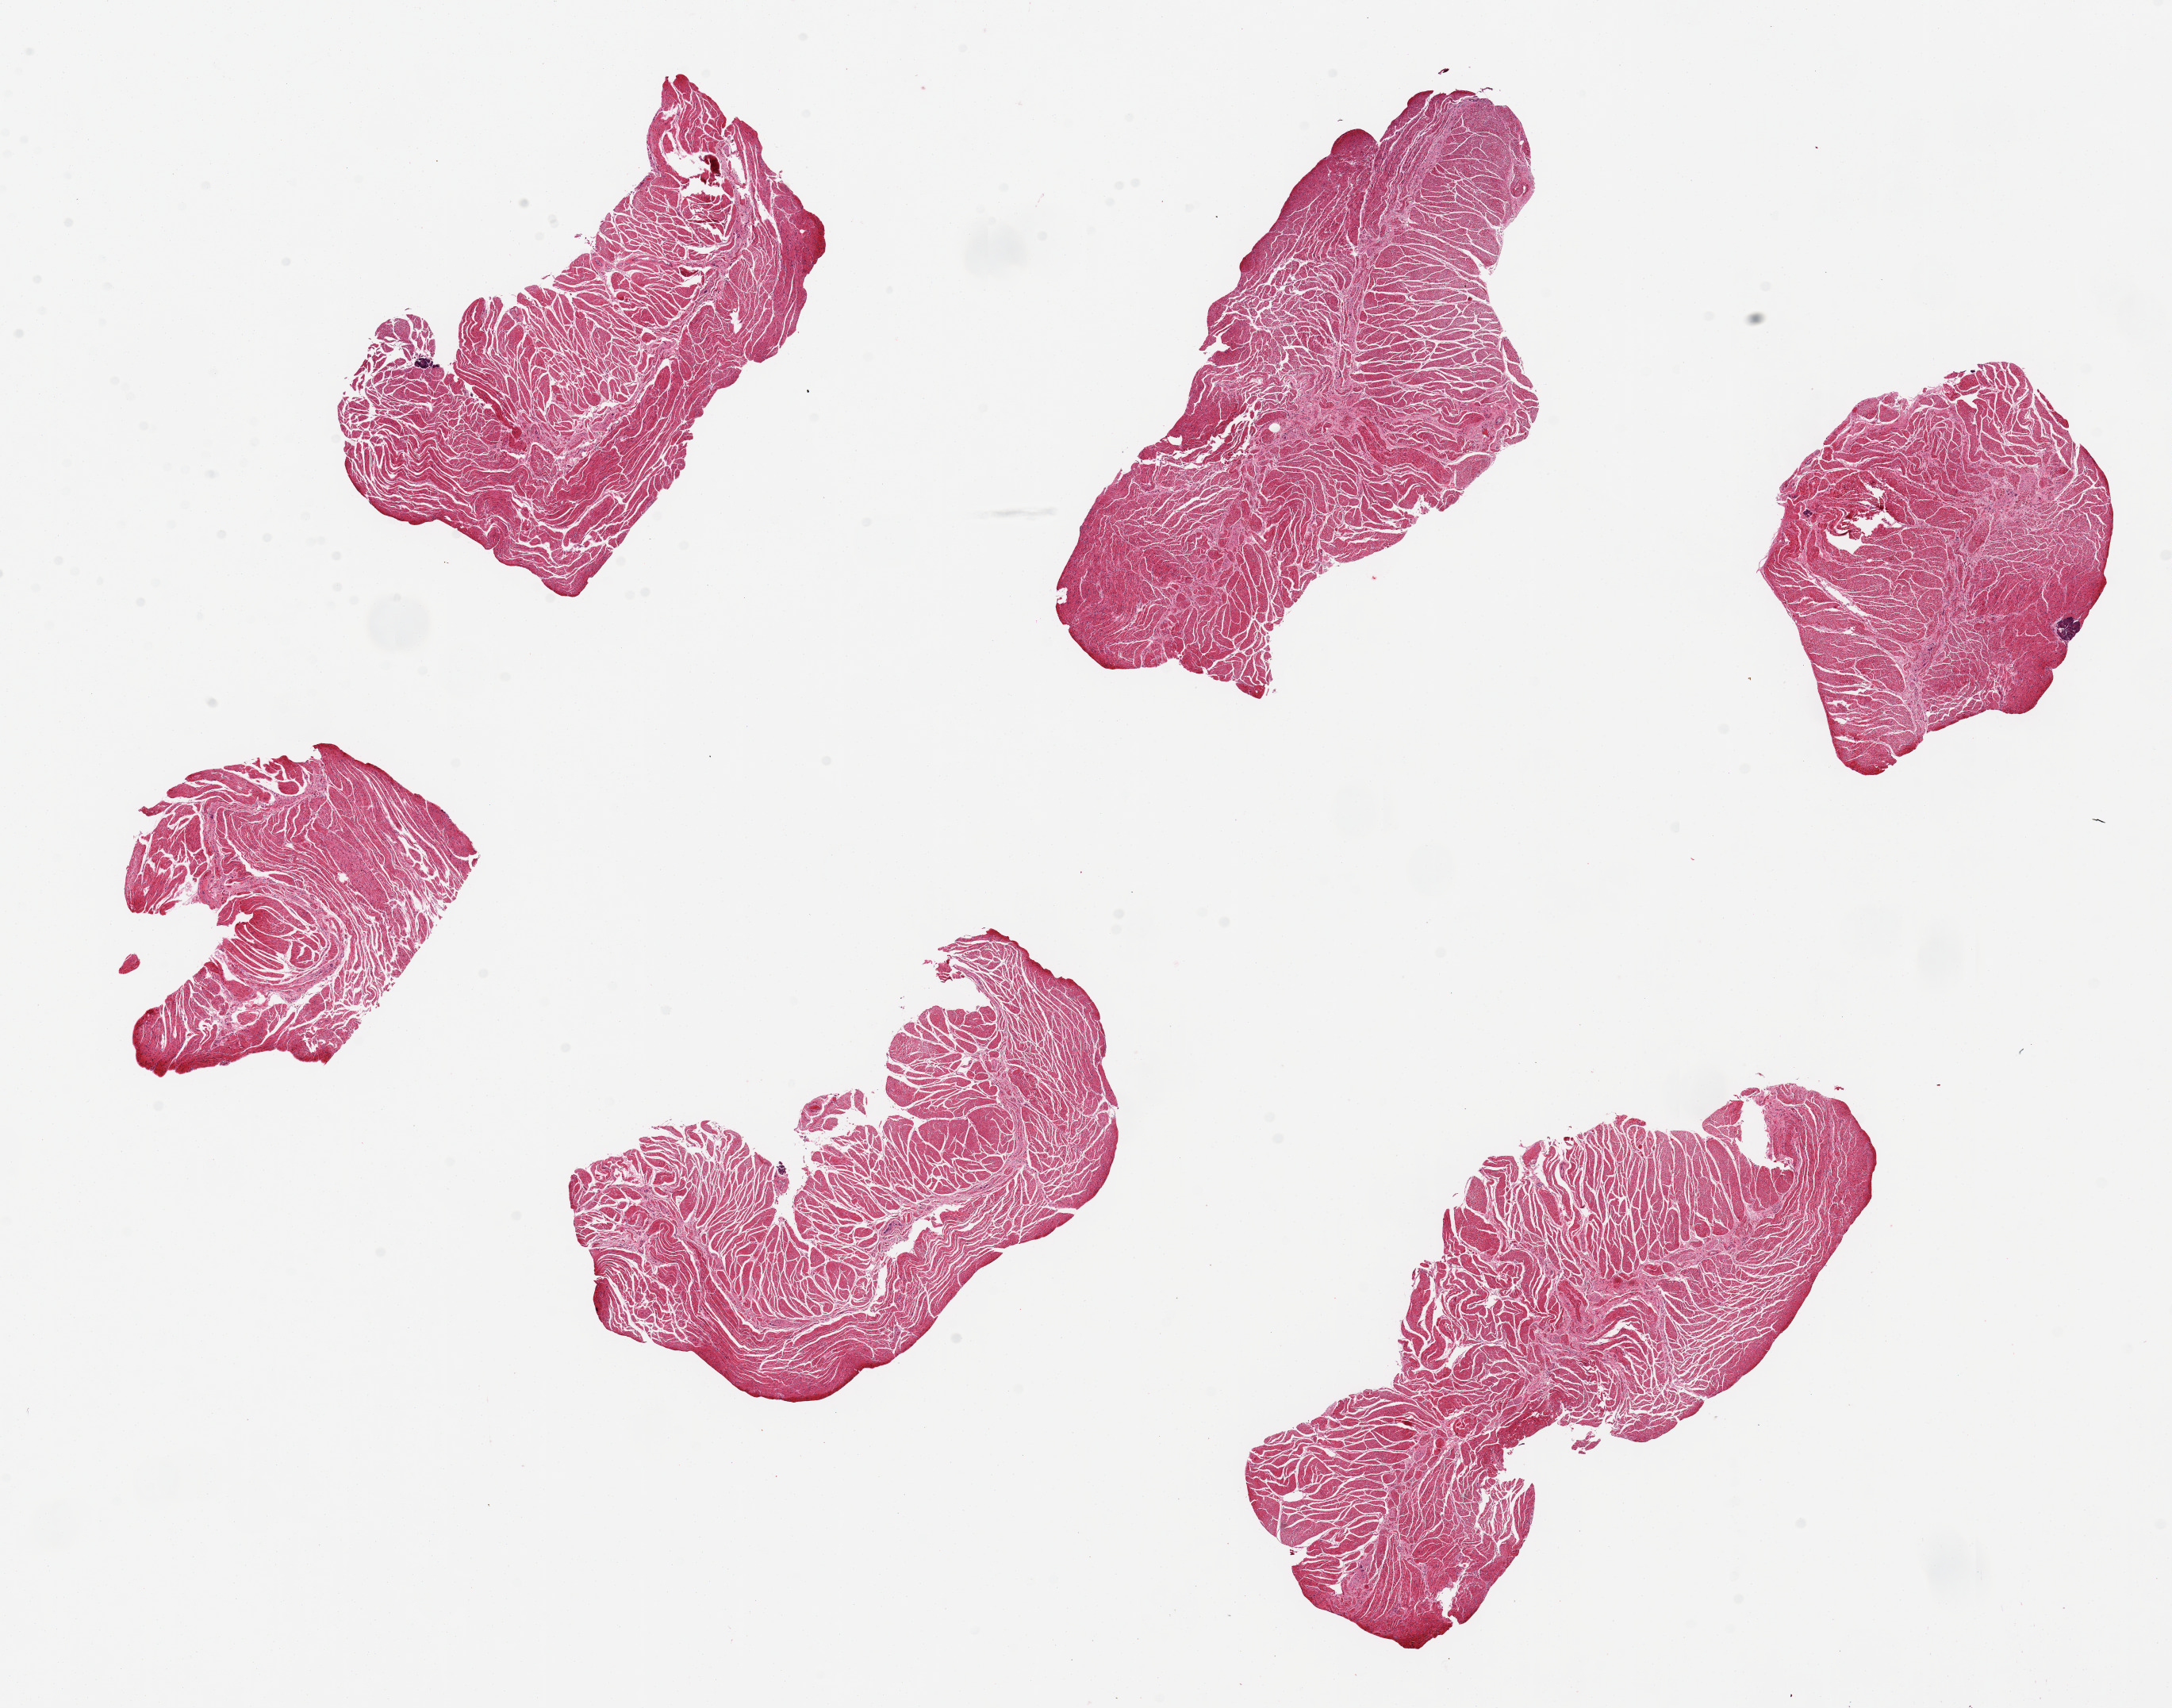
Digitized H&E-stained section, whole scanned area (about 21.7 x 17.0 mm, slide scanned at 20x) shown as a low-resolution overview, PAXgene-fixed, paraffin-embedded tissue, section of esophageal muscle (target tissue), tissue donor sample.
• reviewer comment on this tissue sample: 6 pieces; well dissected